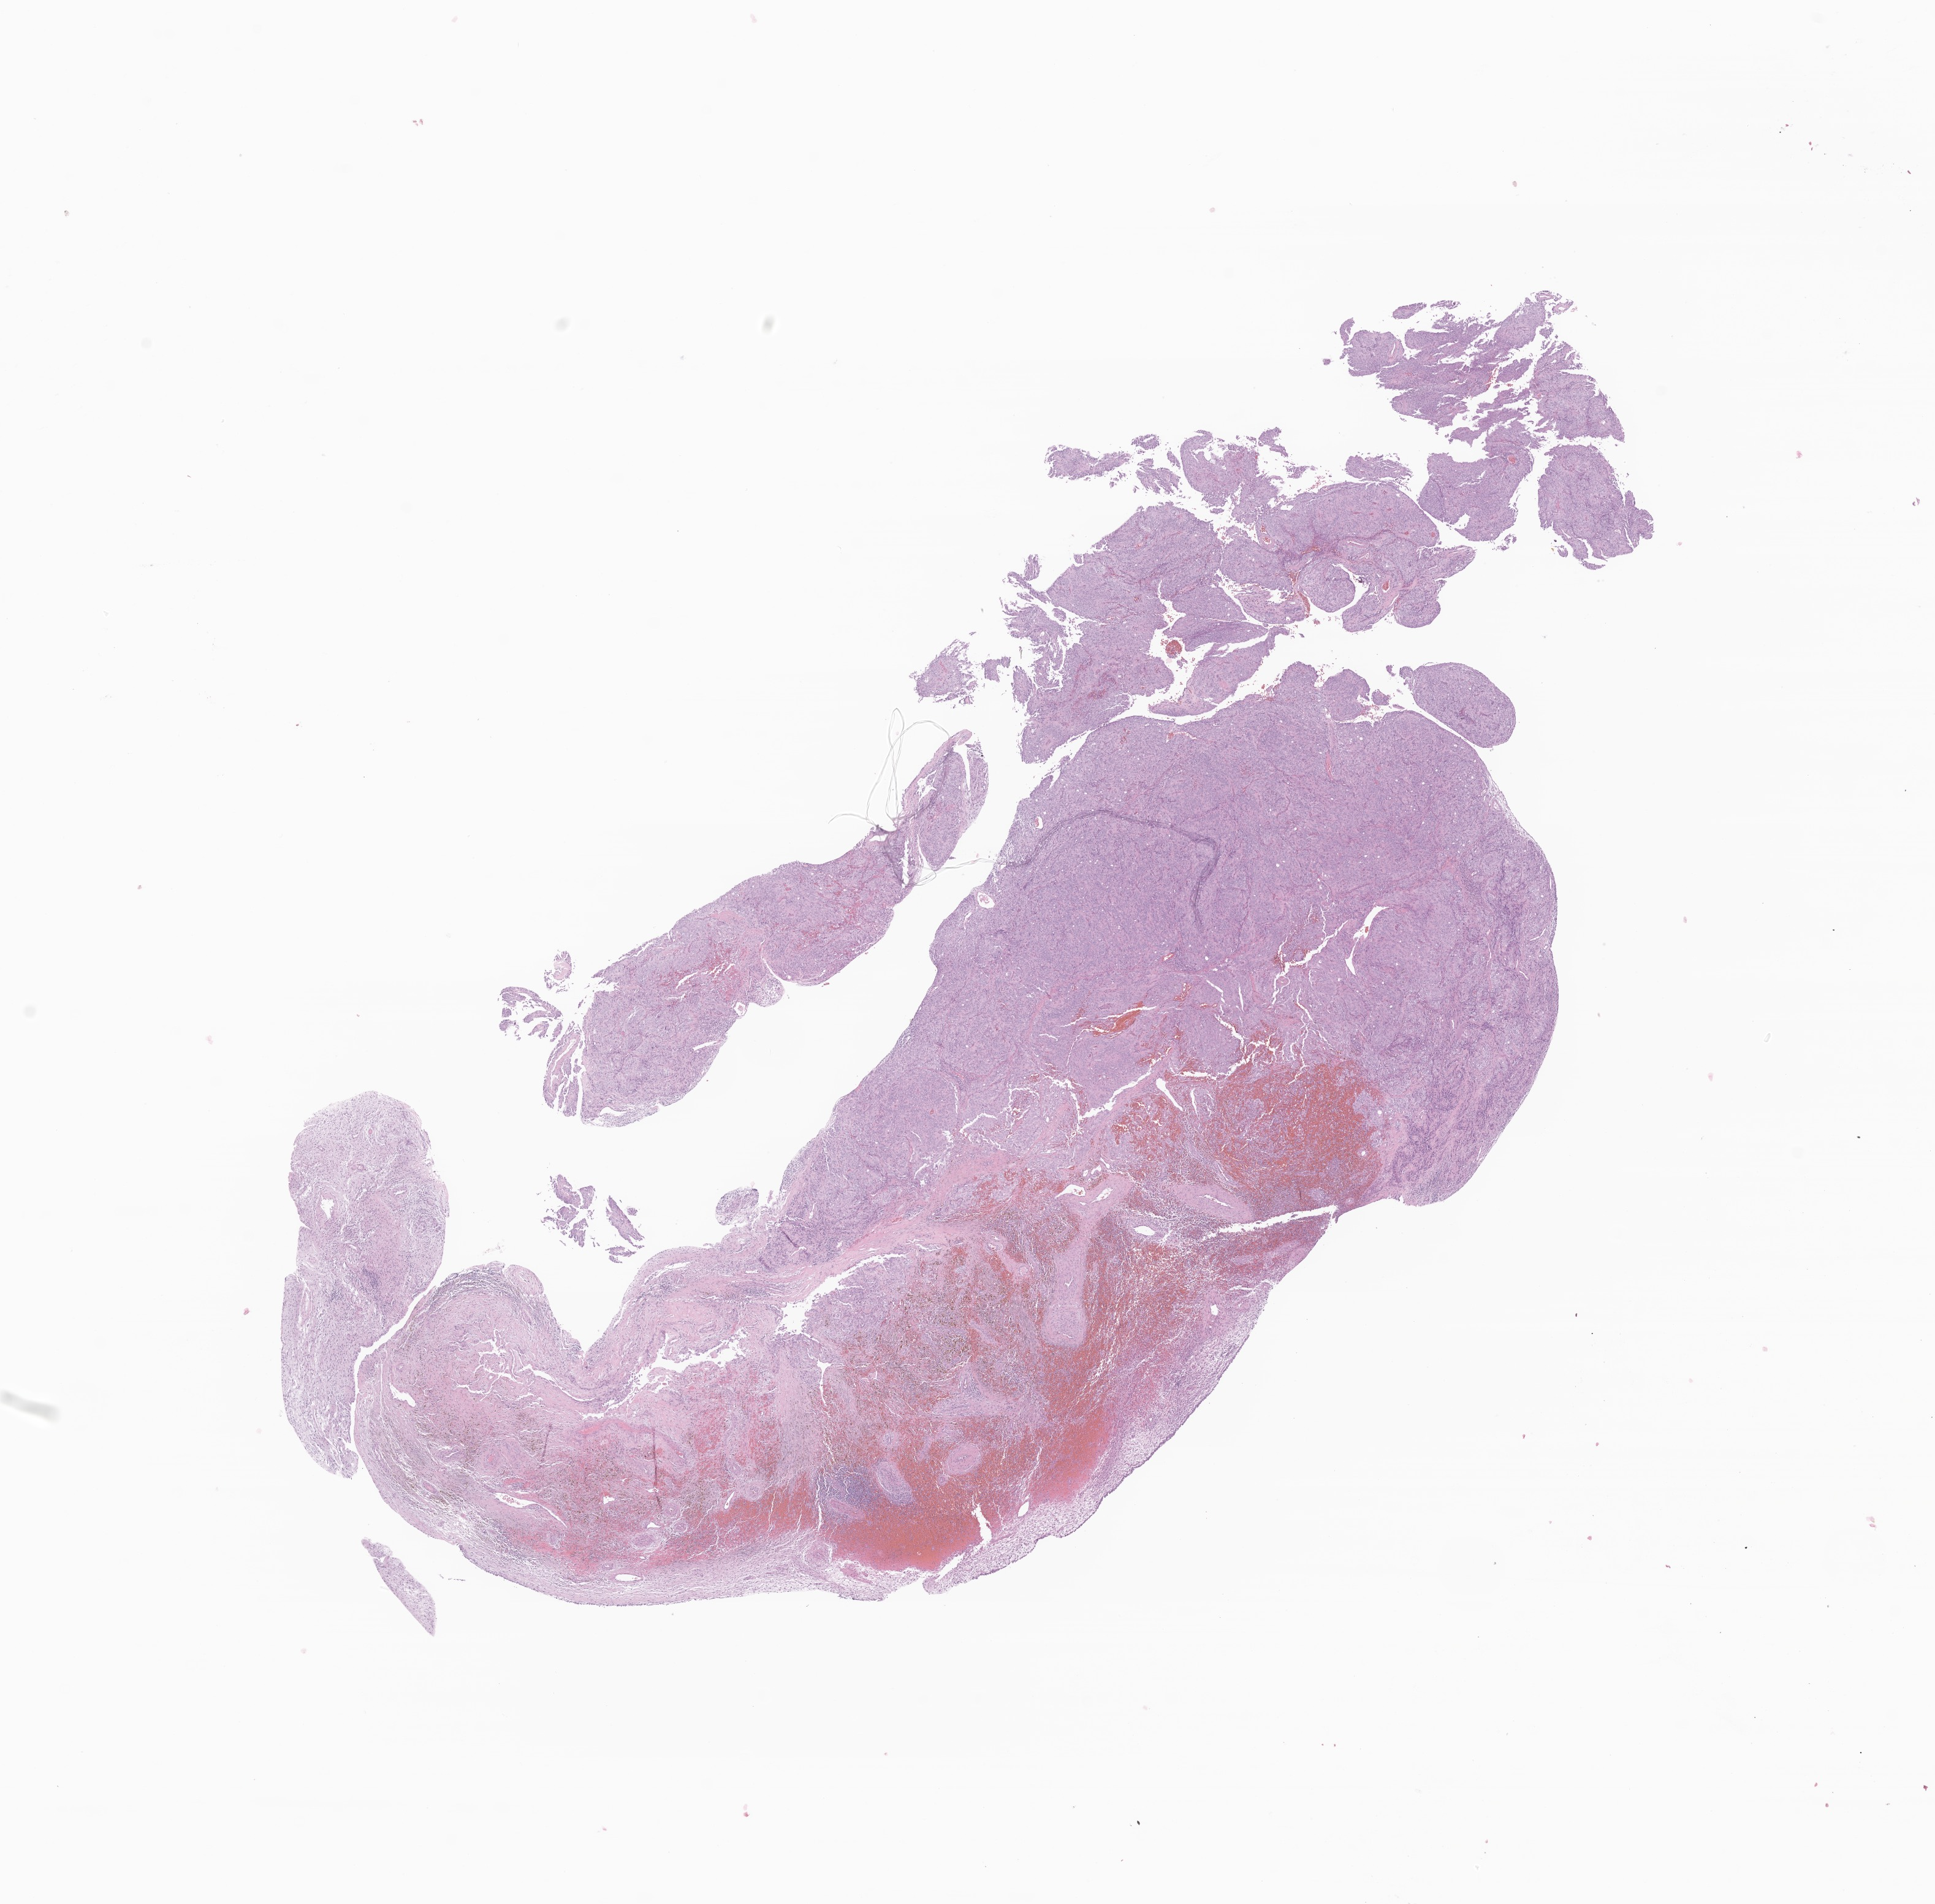
Whole-slide image, hematoxylin and eosin (H&E) stain of tumor tissue from the brain, a low-resolution overview of the entire scanned area, about 13.3 x 13.1 mm. FFPE section. Female patient, age 245 months (20 years 5 months).
Diagnosis (ICD-O-3 morphology term): Meningioma, NOS.